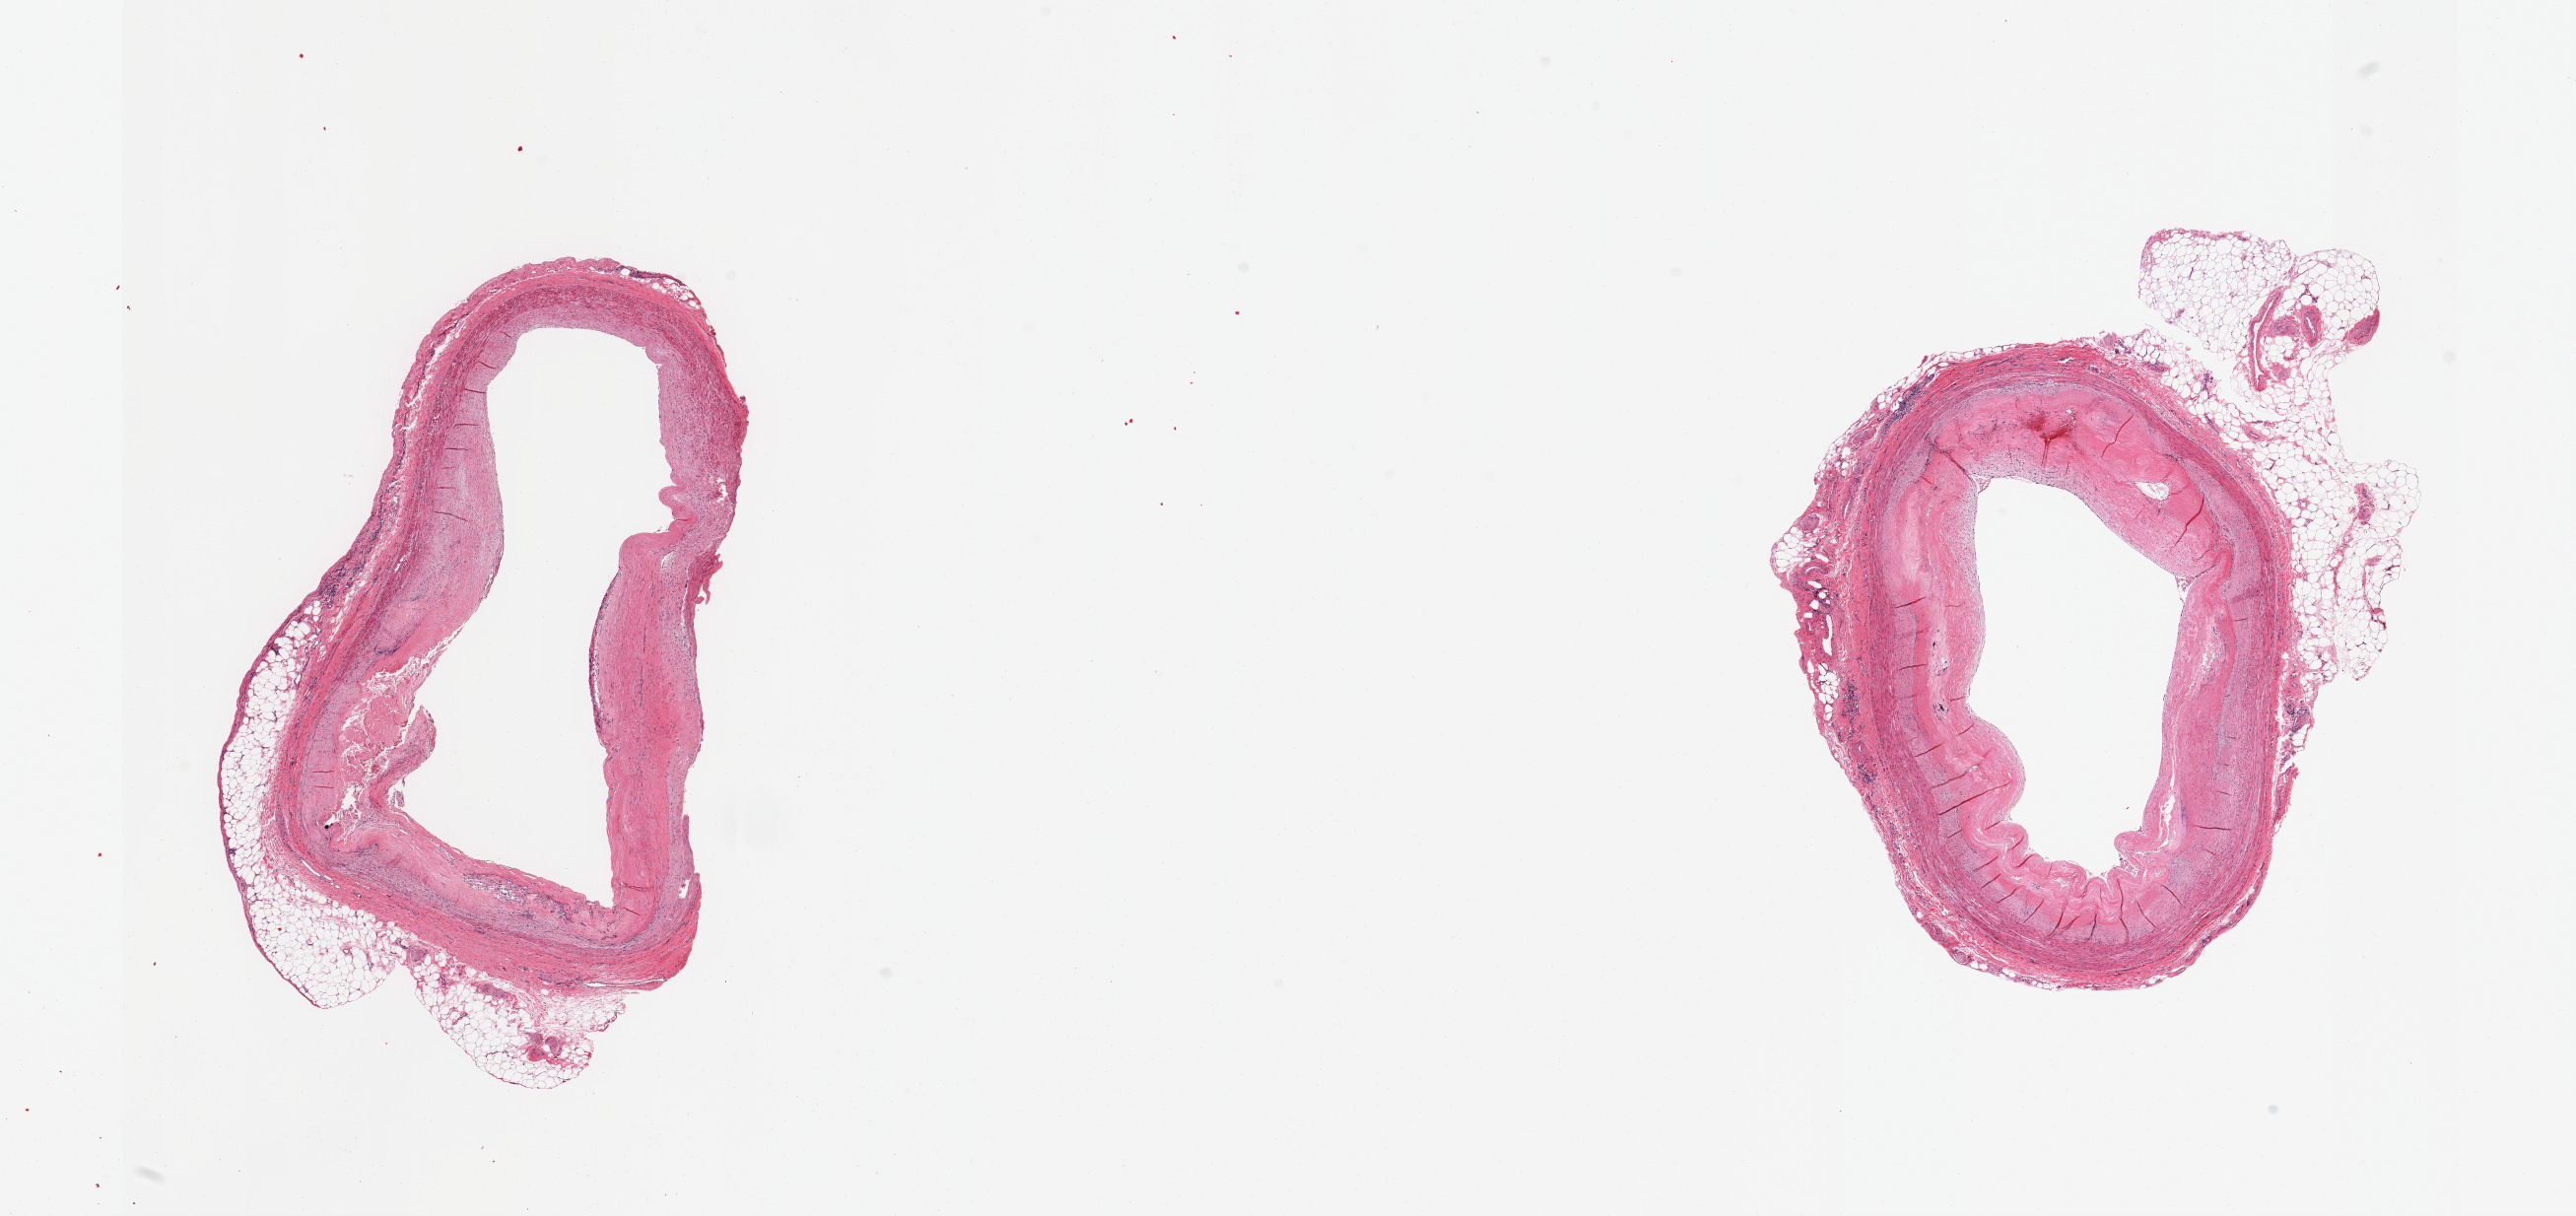
H&E whole-slide image, whole scanned area (about 20.7 x 9.8 mm) shown as a low-resolution overview, PAXgene-fixed, paraffin-embedded tissue, sampled site (target tissue): coronary artery, donor tissue sample. Donor: male.
Review note (as recorded): 2 pieces; severe fibroatherosclerotic plaque but no luminal compromise; 1.5mm external fat.